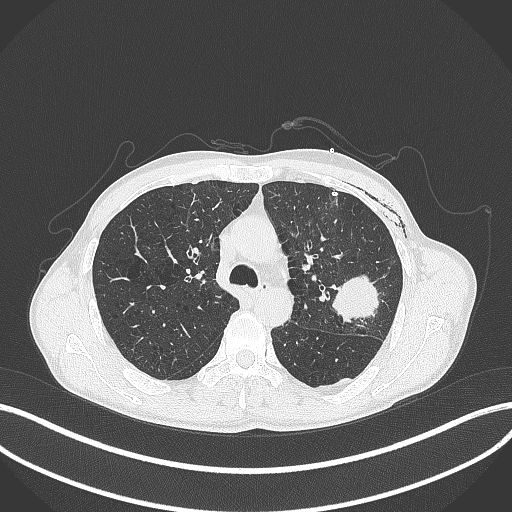
Chest CT, one axial slice. Slice 274 of 457 in the series (ordered by position). Lung window (W 1500 / L -600 HU). 512 × 512 image matrix. Male patient, age 58 years. From the clinical record (not read from this slice): clinical TNM (as recorded): T3 N0 M0.
Outlined on this slice (rectangle marked by the reading radiologist):
- lung tumour (recorded histology: adenocarcinoma): bounding box [x1, y1, x2, y2] px = [330, 271, 381, 323]